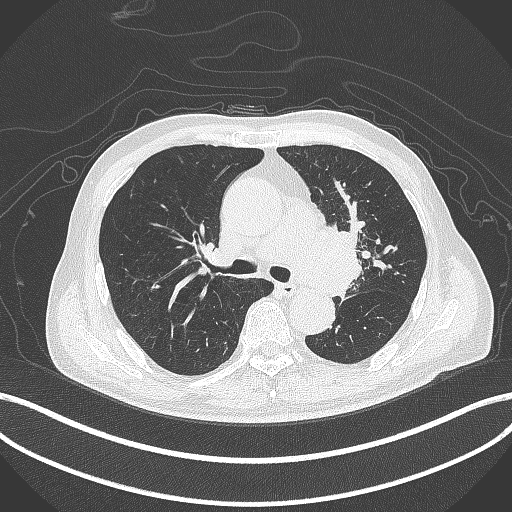
Chest CT, one axial slice; position 274 of 417 along the scan axis; lung window (W 1500 / L -600 HU); 1 mm slice thickness; 512 × 512 image matrix, field of view 400 × 400 mm. Male patient, age 77 years. From the clinical record (not read from this slice): clinical TNM (as recorded): T3 N1 M0.
Outlined on this slice (bounding box drawn by a radiologist):
- lung tumour (recorded histology: adenocarcinoma): bounding box (x1, y1, x2, y2) in pixels: (315, 219, 371, 299)